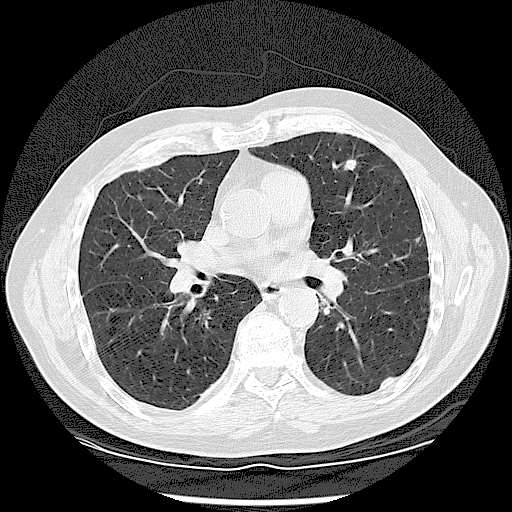
Low-dose screening chest CT, one axial slice; slice 57 of 120 in the series (ordered by position); lung window (W 1500 / L -600 HU); 512 × 512 image matrix.
Outlined on this slice (outlined manually by an expert reader):
- lesion 1 (tumor, upper lobe of left lung): box from (x=345, y=159) to (x=356, y=172) px